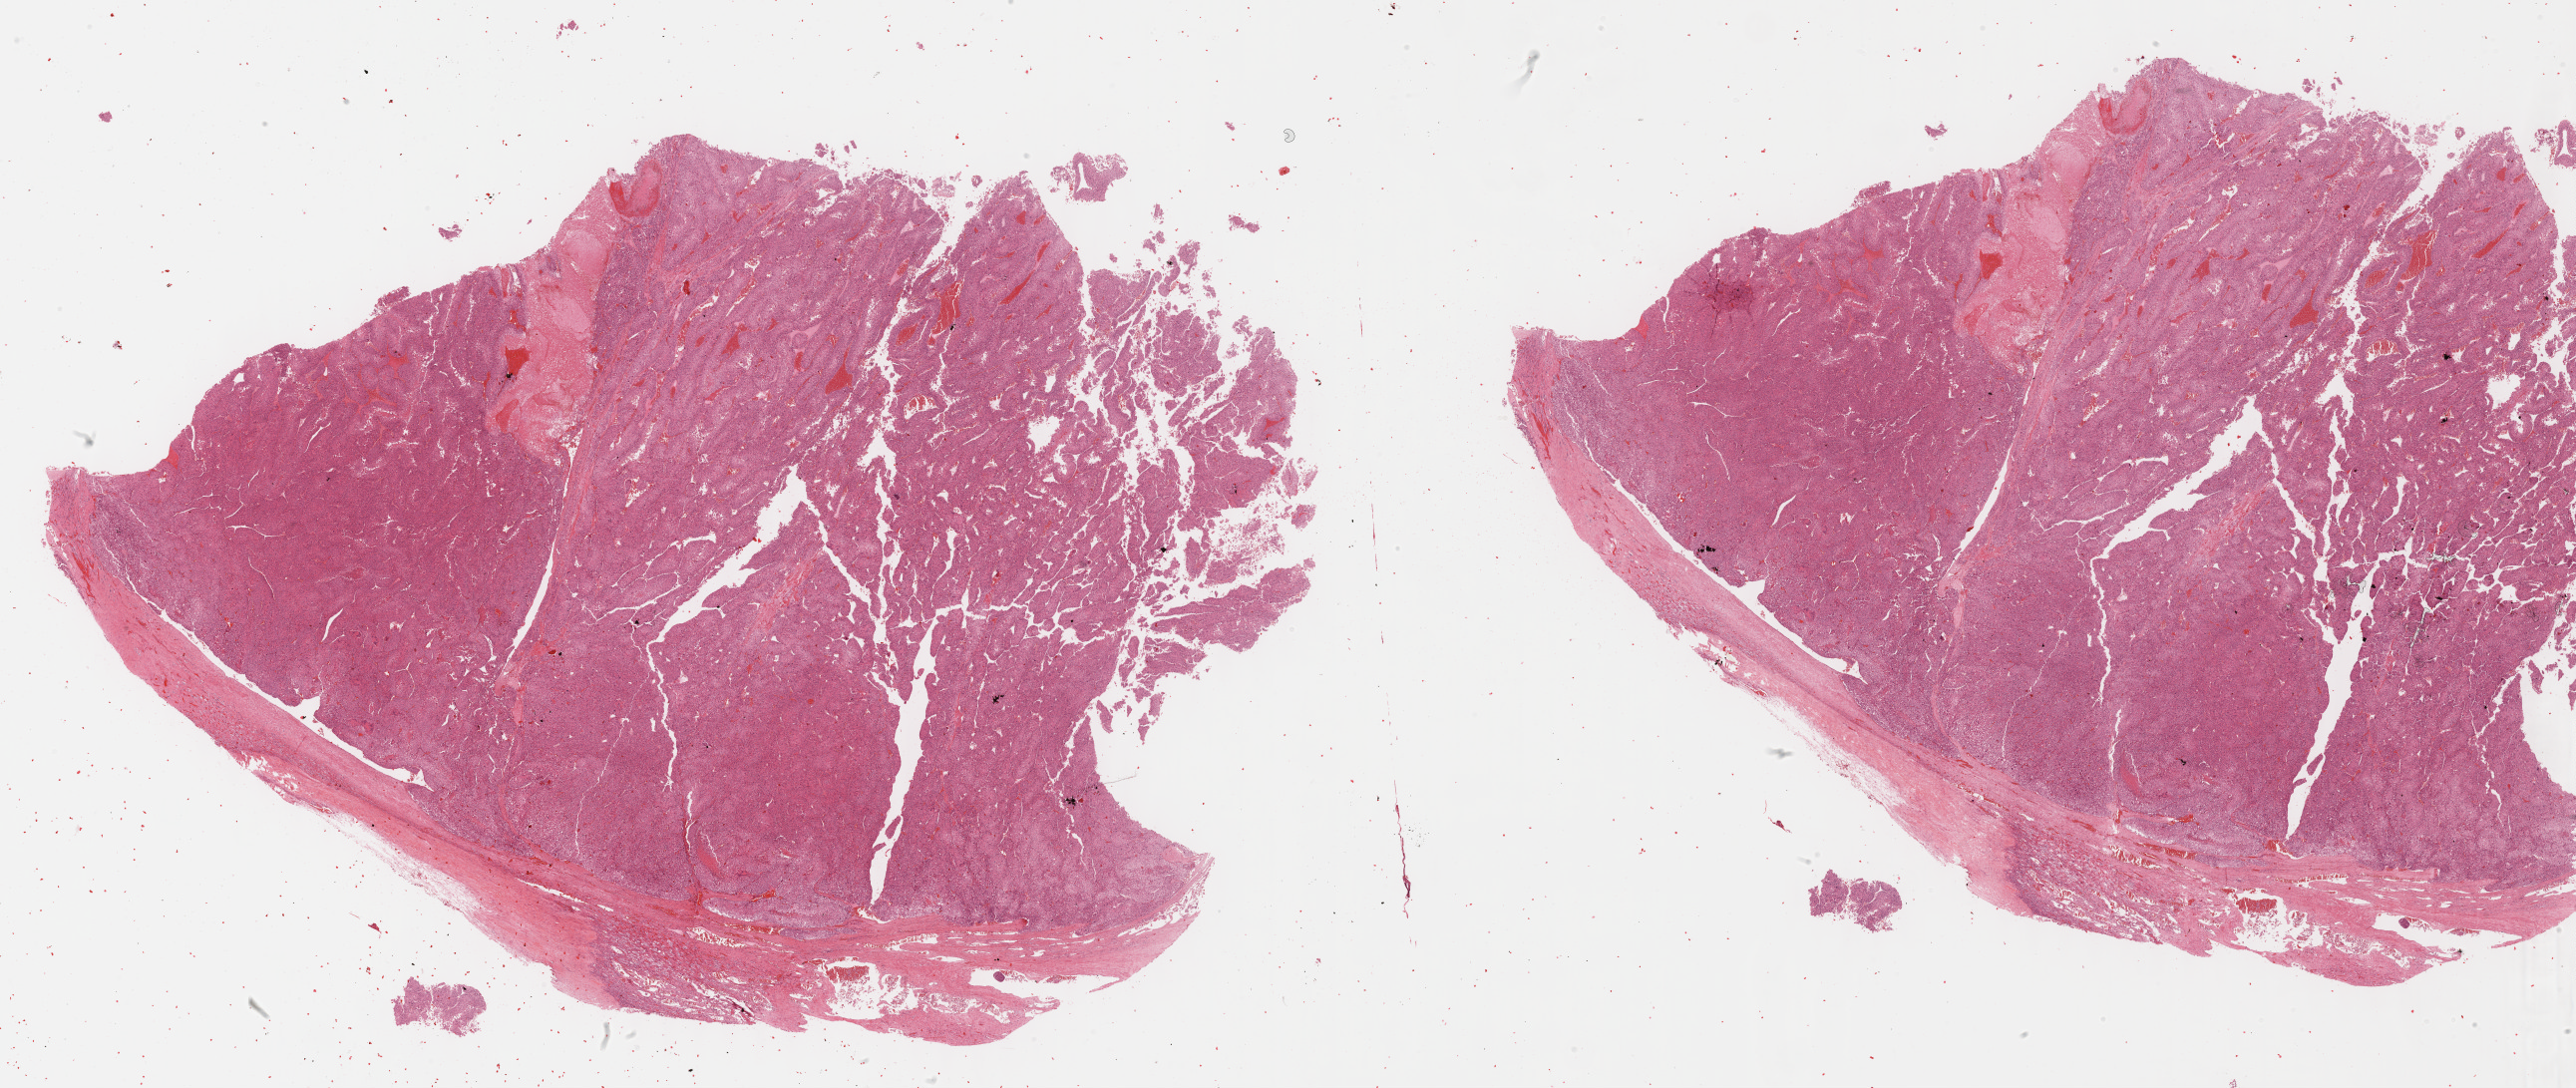
Digitized H&E-stained tissue section (whole slide), low-resolution overview of the scanned area, about 41.7 x 17.6 mm; formalin-fixed paraffin-embedded (FFPE) diagnostic section; primary tumour sample from the adrenal cortex. Patient: female, age at initial diagnosis 53 years.
Histologic diagnosis: Adrenal cortical carcinoma (cortex of adrenal gland).